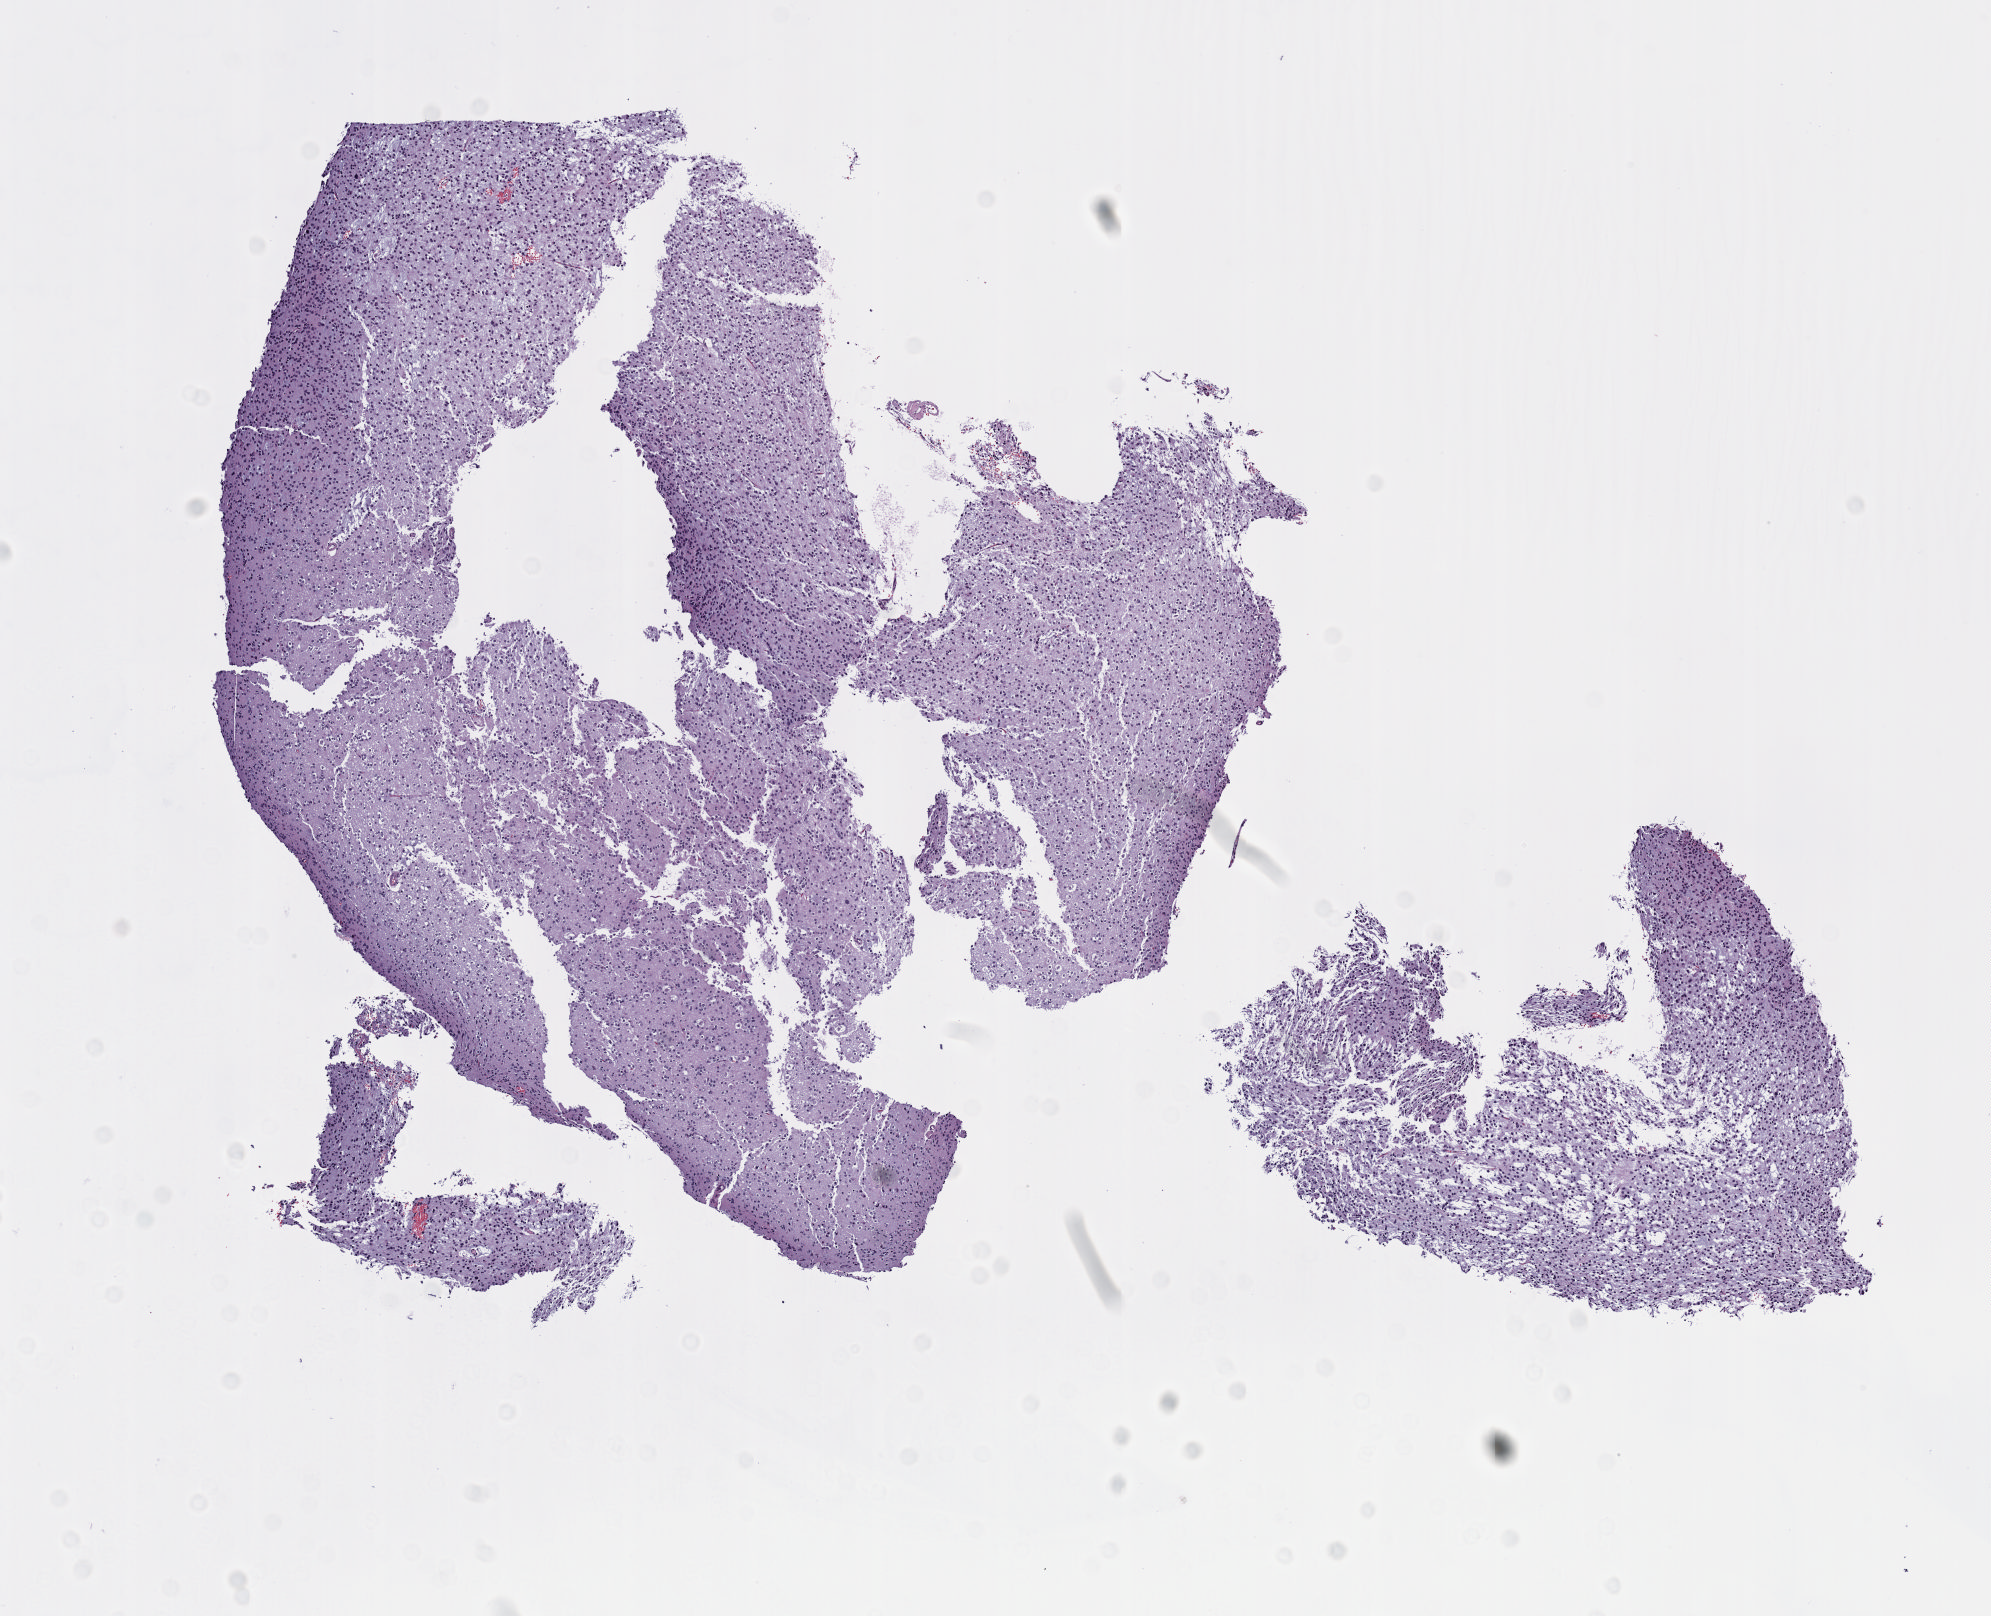
H&E-stained whole-slide image — low-resolution overview of the scanned area, about 8.1 x 6.5 mm; formalin-fixed paraffin-embedded (FFPE) diagnostic section; brain, primary tumour sample. Female, age 50 years at initial diagnosis. Histologic grade: G2 (moderately differentiated).
Diagnosis: Oligodendroglioma, NOS. Laterality: right.